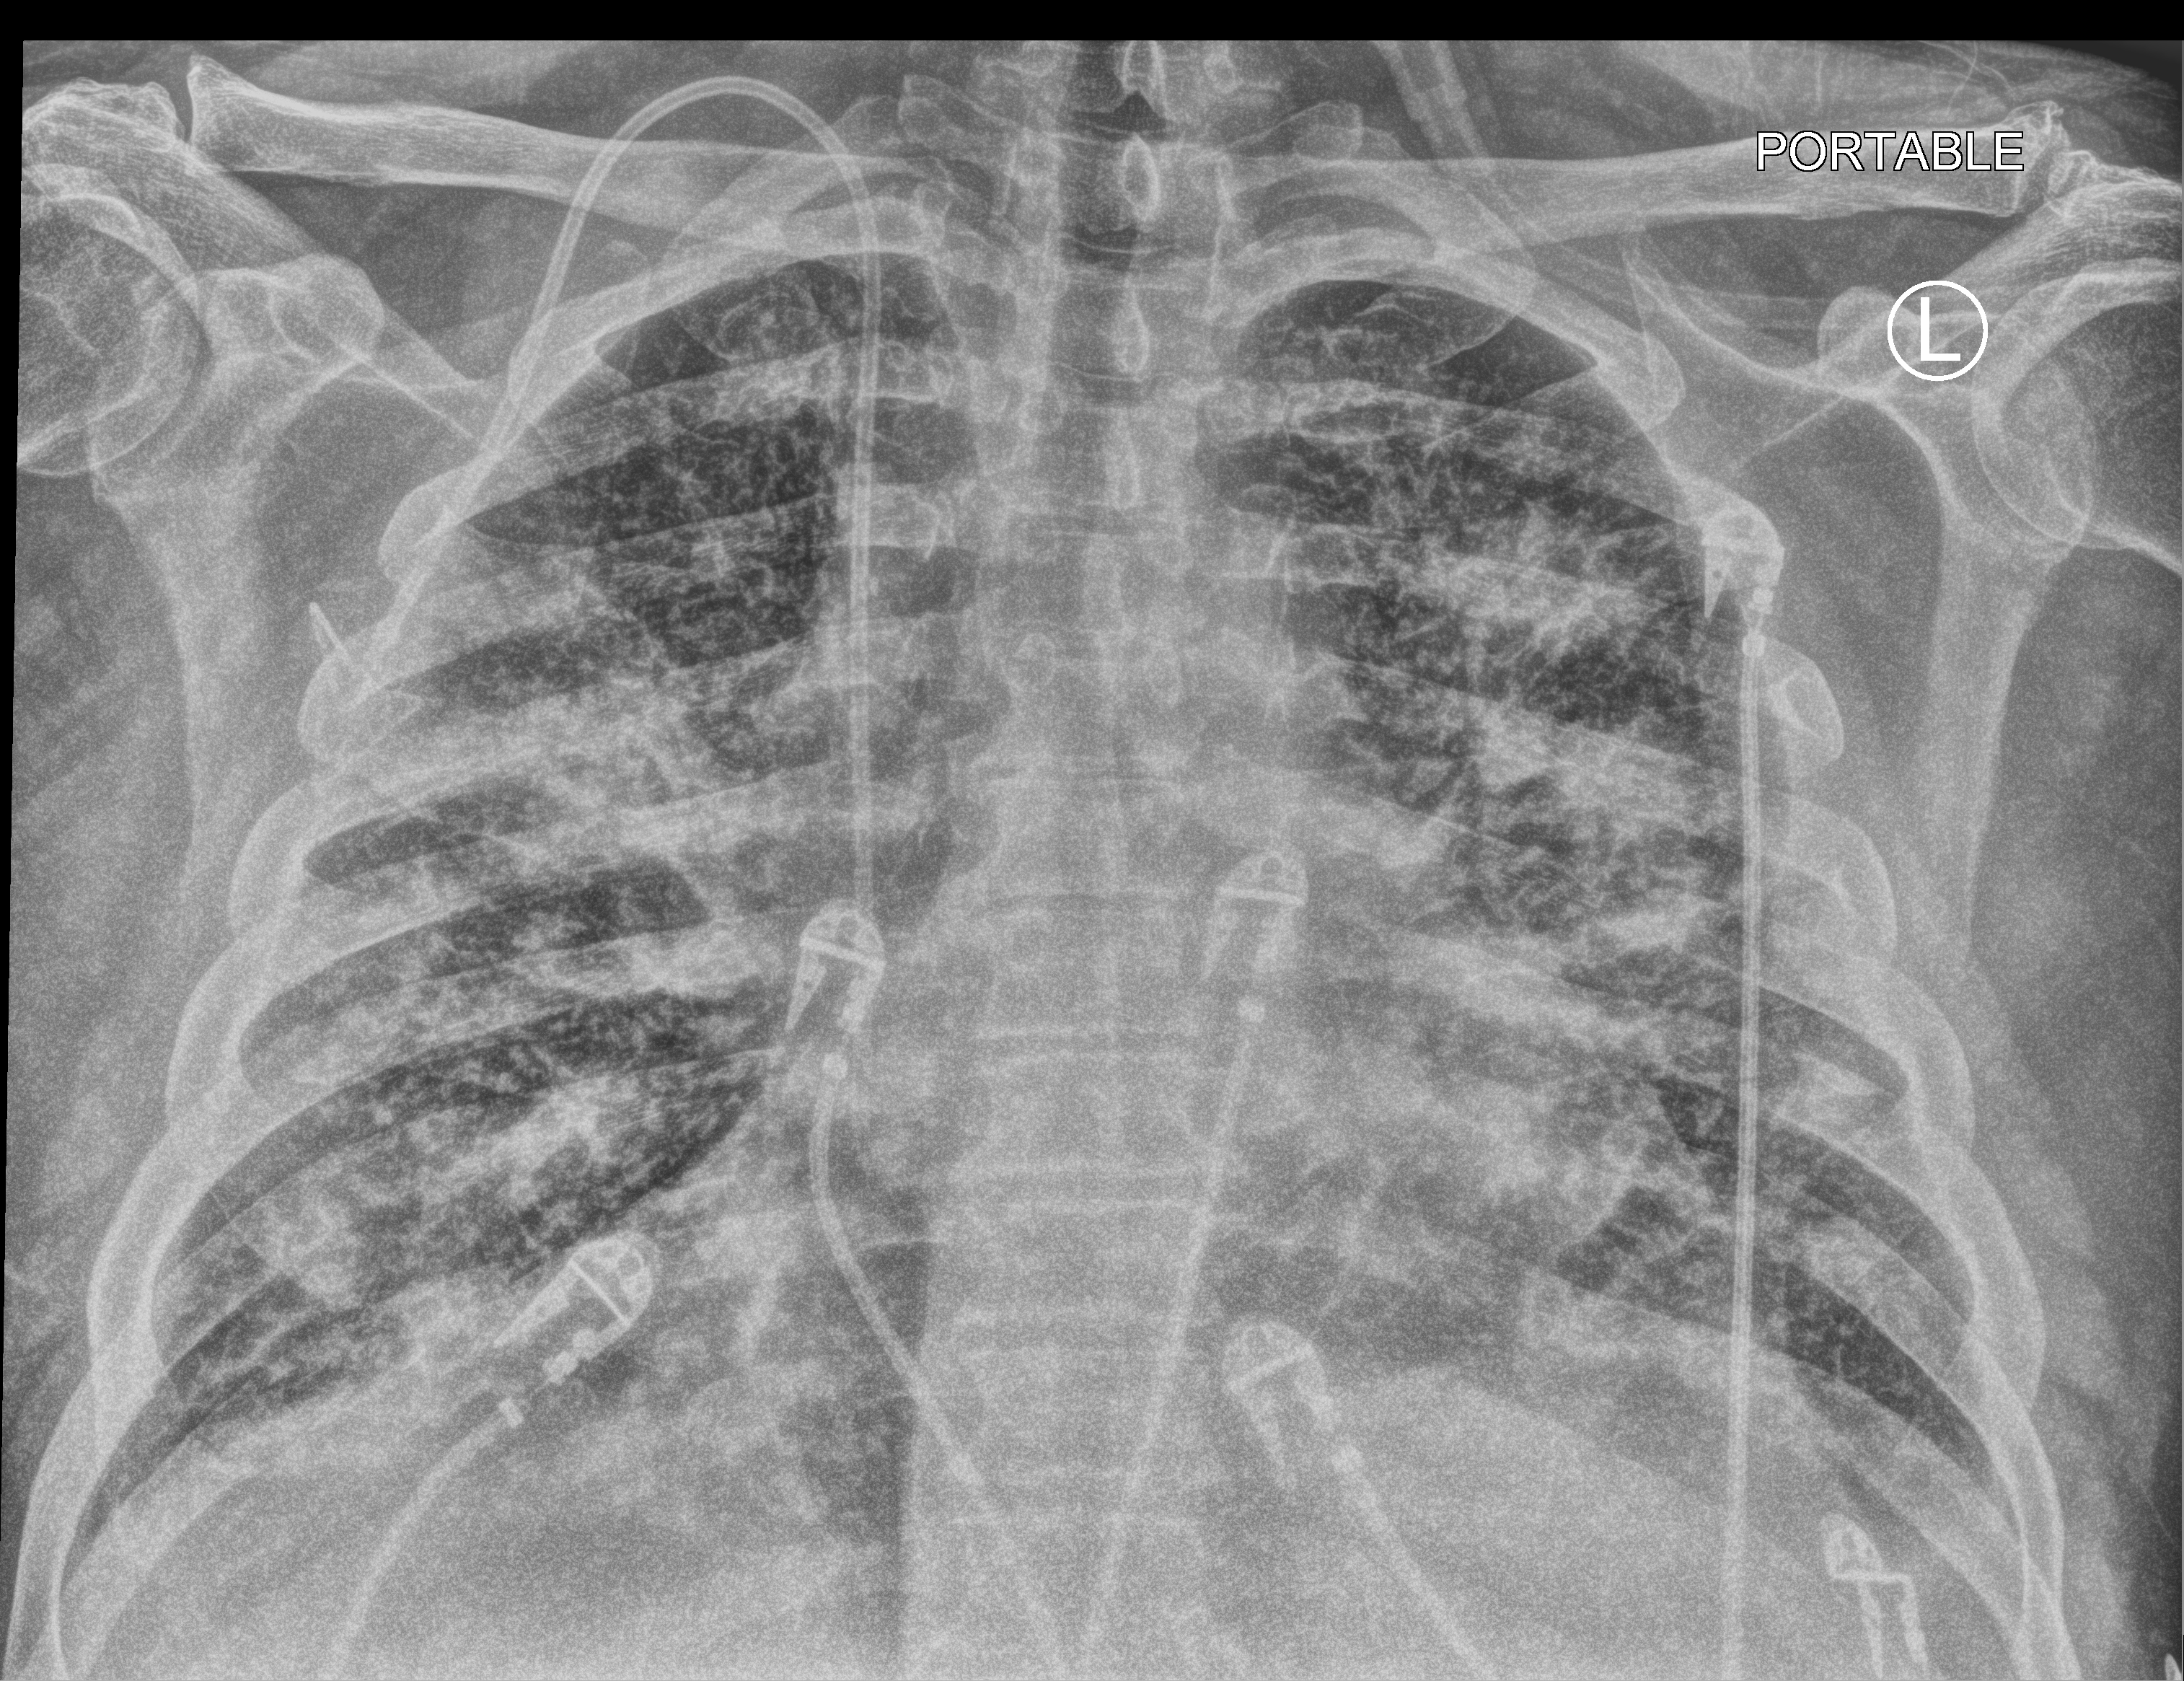
Bedside chest radiograph (computed radiography), anteroposterior (AP) projection. Patient hospitalised with COVID-19; male, aged 60–74 years.
From the hospital-stay record, not from the radiograph (when in the stay this image was taken is not recorded): mechanically ventilated during this hospital stay: no.